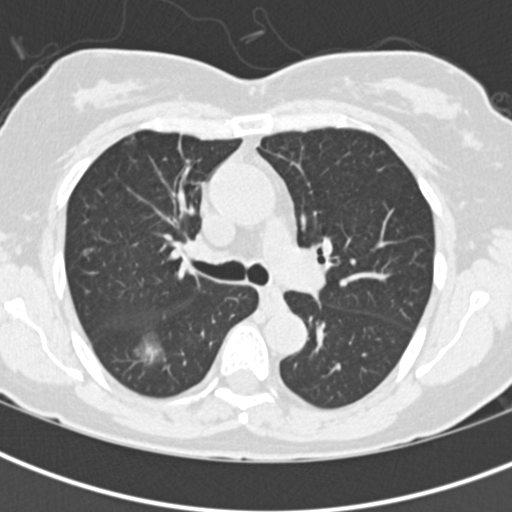
Low-dose screening chest CT, one axial slice. Slice 136 of 198 in the series (ordered by position). 120 kVp. Lung window (W 1500 / L -600 HU). 2 mm slice thickness. 512 × 512 image matrix.
Annotated regions visible in this slice (outlined manually by an expert reader):
- lesion 1 (tumor, lower lobe of right lung): bounding box [x1, y1, x2, y2] px = [136, 333, 165, 366]